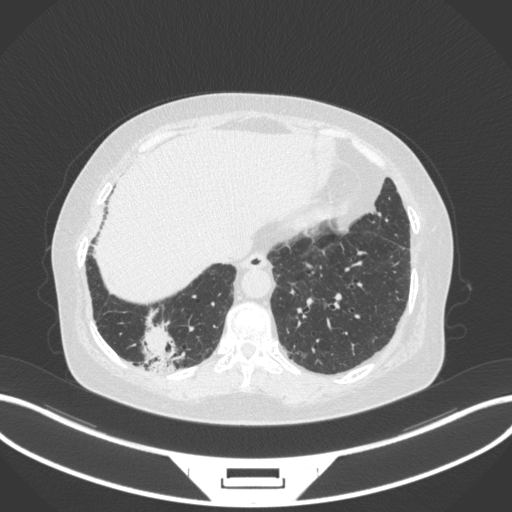
Chest CT, one axial slice; position 33 of 303 along the scan axis; 120 kVp; lung window (W 1500 / L -600 HU); 1 mm slice thickness; 512 × 512 image matrix. Patient: female, 65 years. Case-level facts recorded for this patient, not image findings: clinical TNM (as recorded): T2b N1 M0; histopathological grade: G1.
Outlined on this slice (rectangle marked by the reading radiologist):
- lung tumour (recorded histology: adenocarcinoma): bounding box (x1, y1, x2, y2) in pixels: (135, 309, 180, 373)